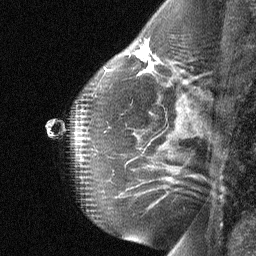
Breast MRI (dynamic contrast-enhanced), one sagittal slice; position 41 of 64 along the scan axis; dynamic contrast-enhanced study with each time point stored as its own series, time point 2 of 3 at this slice position (early post-contrast, ordered by acquisition time); 1.5 T; TE 4.8 ms, TR 27 ms; 2 mm slice thickness; 256 × 256 image matrix, field of view 180 × 180 mm. Patient: female, 51 years. From the clinical record (not read from this slice): setting: breast cancer imaged before/during neoadjuvant chemotherapy; receptor status: HR-positive, HER2-negative.
Annotated regions visible in this slice (semi-automatically segmented with operator editing):
- analysis volume of interest (the breast-tissue region the enhancement analysis was run in; not a lesion): bounding box (x1, y1, x2, y2) in pixels: (81, 35, 179, 103)
- tumour enhancement mask (voxels above the 90 % enhancement threshold inside the analysis volume of interest): (136, 41, 152, 70)